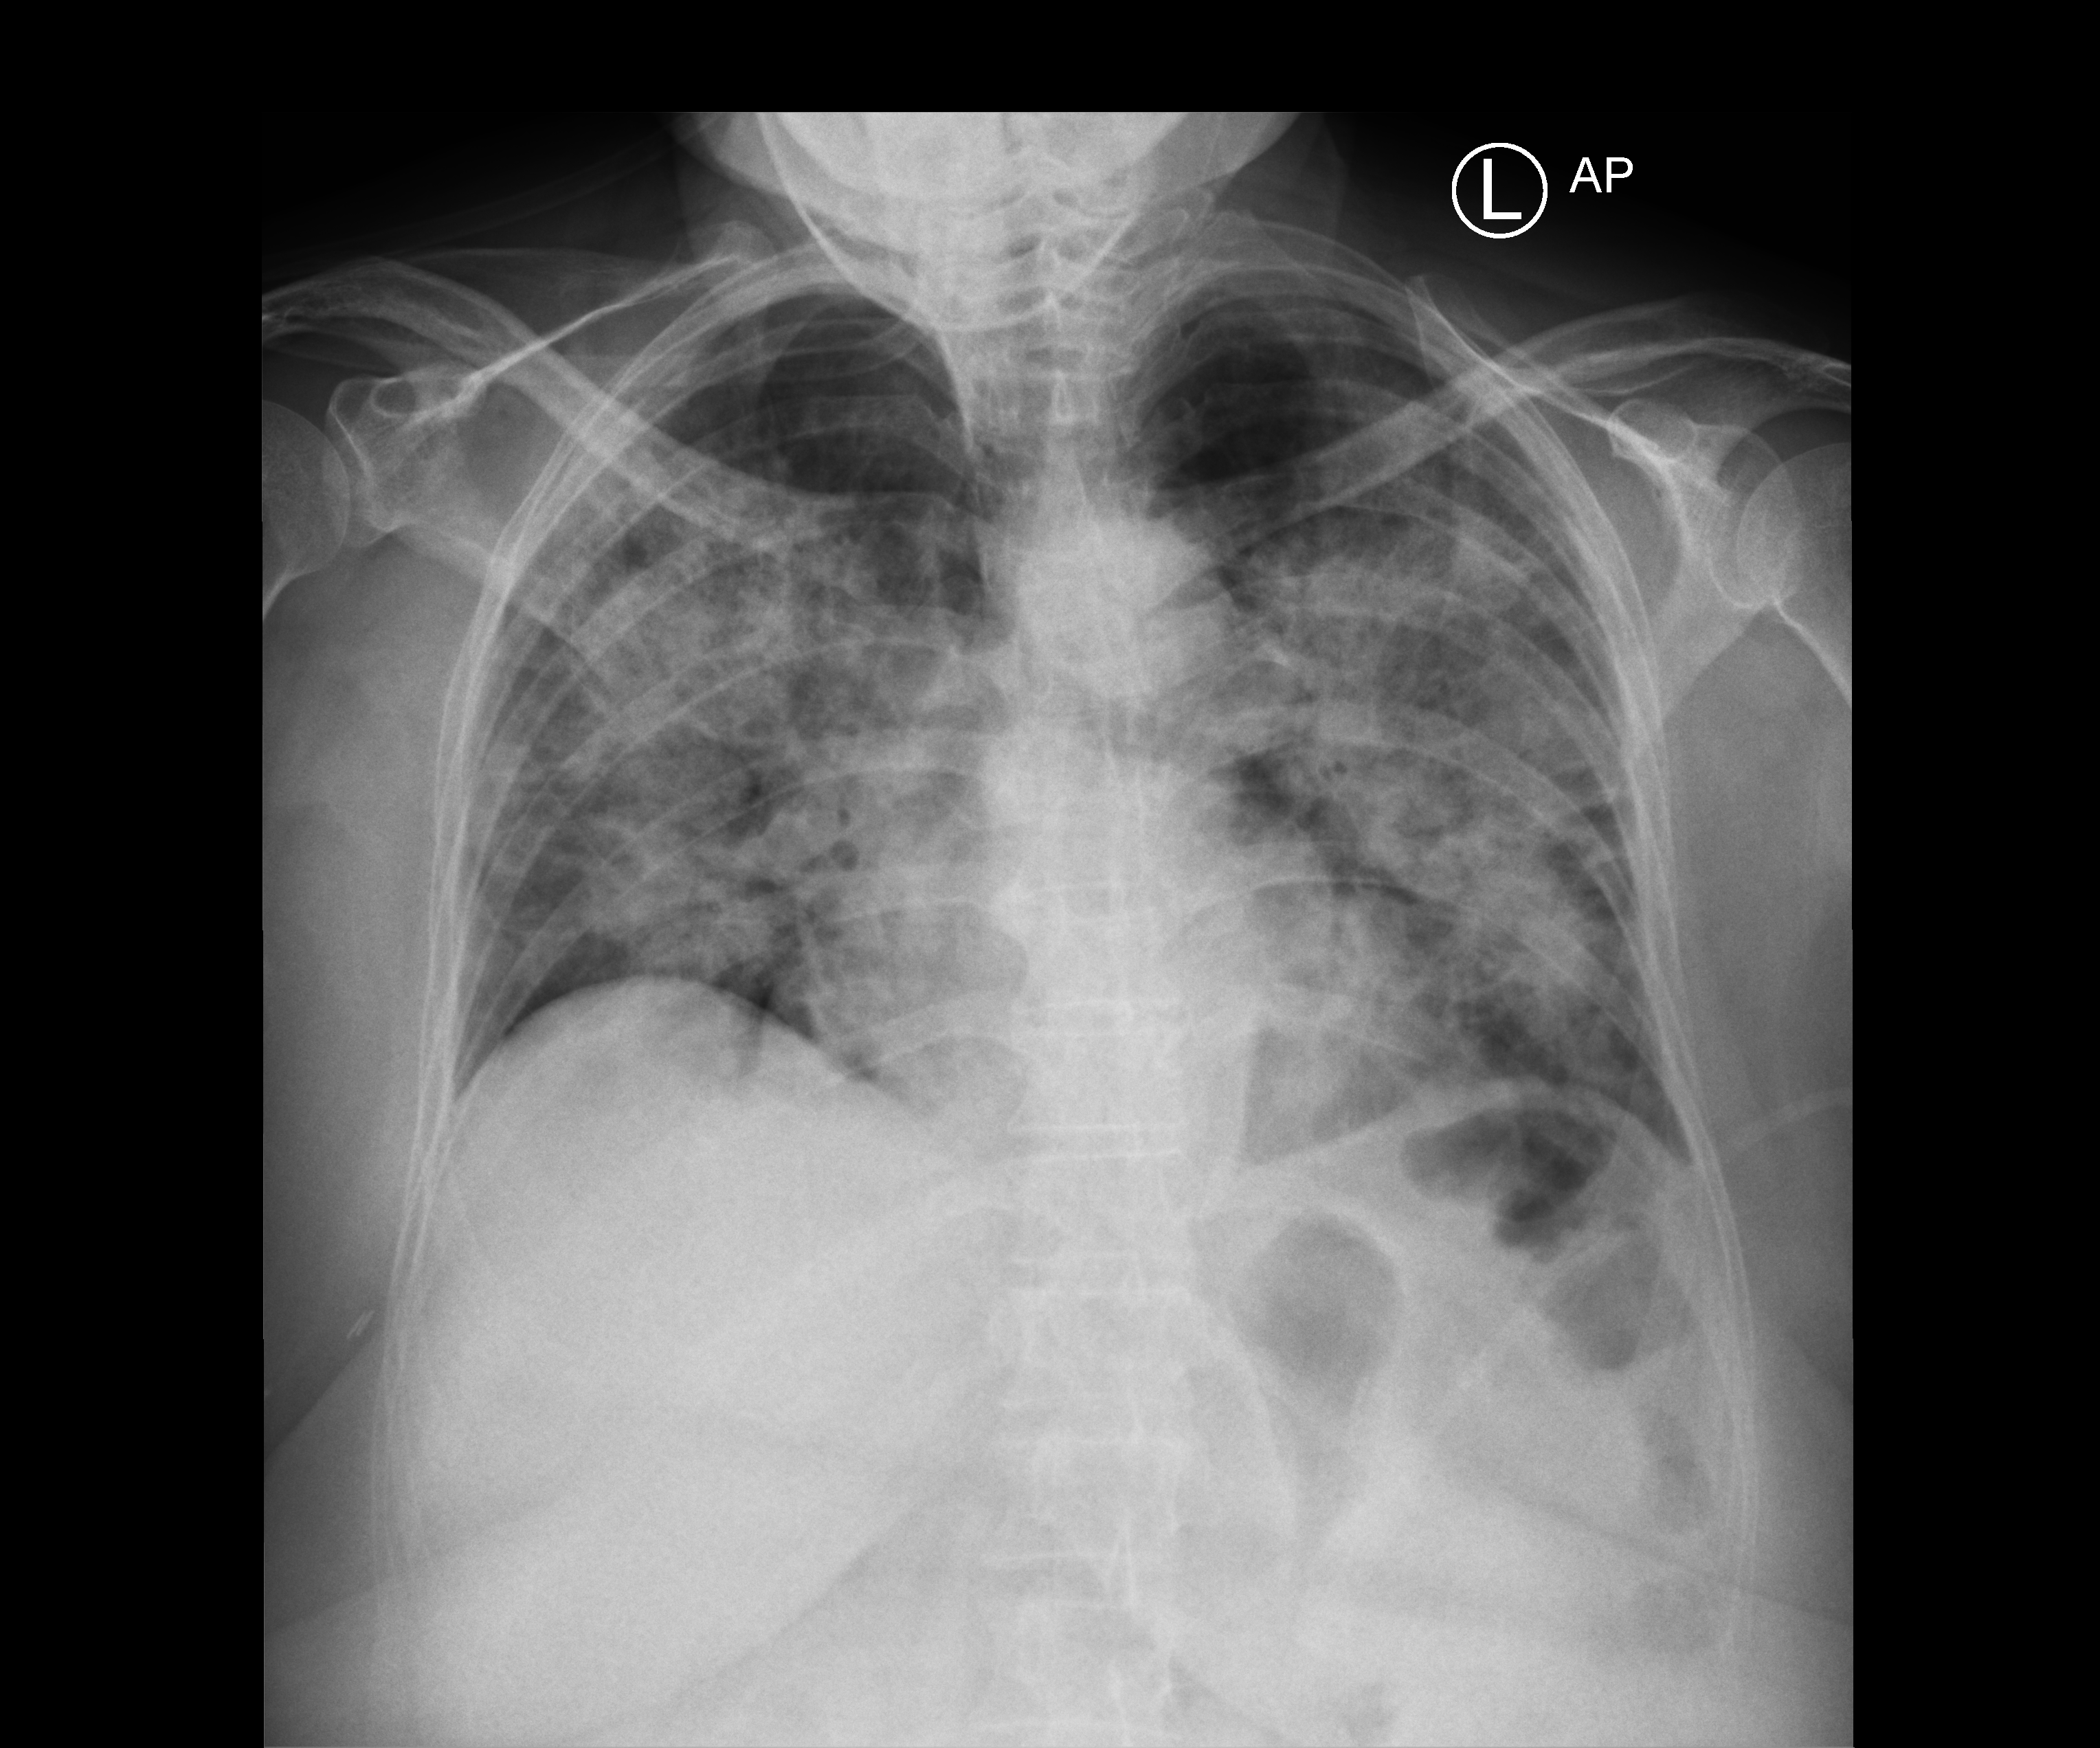
Bedside chest radiograph (computed radiography), anteroposterior (AP) projection. Patient hospitalised with COVID-19; female, aged 60–74 years.
Admission-level facts for this patient (not findings on this image; timing relative to this image not recorded):
- mechanically ventilated during this hospital stay: no
- admitted to intensive care during this hospital stay: no